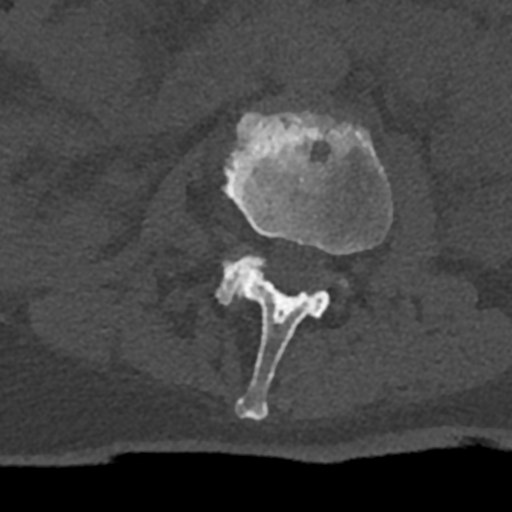
CT including the spine, one axial slice; position 362 of 797 along the scan axis; 120 kVp; bone window (W 1800 / L 400 HU); 512 × 512 image matrix, field of view 160 × 160 mm. Patient: male, 74 years. Case-level facts recorded for this patient, not image findings: primary cancer: renal.
Structures marked on this image (semi-automatically segmented with operator editing):
- L2 vertebra: box from (x=223, y=110) to (x=393, y=421) px
- L3 vertebra: (x=217, y=254)–(x=344, y=305)